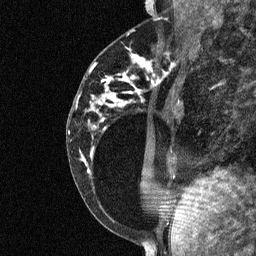
Breast MRI (dynamic contrast-enhanced), one sagittal slice. Slice 27 of 64 in the series (ordered by position). Dynamic contrast-enhanced study with each time point stored as its own series, time point 2 of 3 at this slice position (early post-contrast, ordered by acquisition time). 1.5 T. TE 4.8 ms, TR 27 ms. 2 mm slice thickness. 256 × 256 image matrix, field of view 180 × 180 mm. Patient: female, 34 years. Case-level facts recorded for this patient, not image findings: setting: breast cancer imaged before/during neoadjuvant chemotherapy; receptor status: HR-positive, HER2-negative.
Outlined on this slice (semi-automatic segmentation, software-assisted and operator-edited):
- analysis volume of interest (the breast-tissue region the enhancement analysis was run in; not a lesion): bounding box (x1, y1, x2, y2) in pixels: (78, 44, 181, 191)
- tumour enhancement mask (voxels above the 90 % enhancement threshold inside the analysis volume of interest): (103, 88, 117, 102)